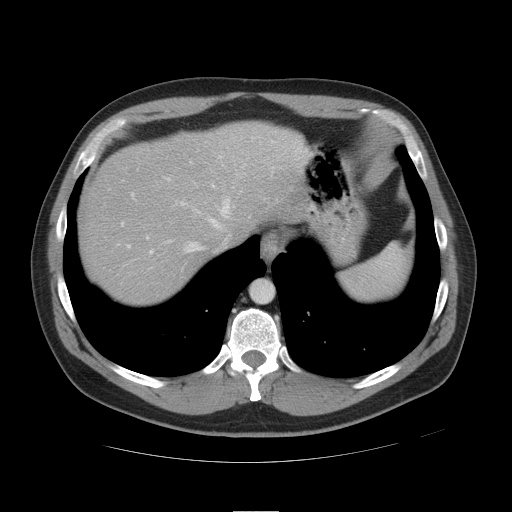
Contrast-enhanced abdominal CT, one axial slice. Slice 39 of 49 in the series (ordered by position). Reconstruction kernel STANDARD. Intravenous contrast given. Soft-tissue window (W 400 / L 40 HU). 5 mm slice thickness. 512 × 512 image matrix, field of view 425 × 425 mm. Male patient, age 52 years. Case-level facts recorded for this patient, not image findings: diagnosis: colorectal cancer liver metastases, imaged before liver resection; multiple liver metastases: yes; largest metastasis: 5.1 cm; chemotherapy before resection: yes.
Annotated regions visible in this slice (outlined manually by an expert reader):
- hepatic veins: bounding box (x1, y1, x2, y2) in pixels: (127, 142, 261, 252)
- liver: (83, 124, 303, 304)
- planned liver remnant (the part of the liver to remain after resection): (135, 125, 302, 234)
- portal vein (with intrahepatic branches): (121, 178, 170, 254)